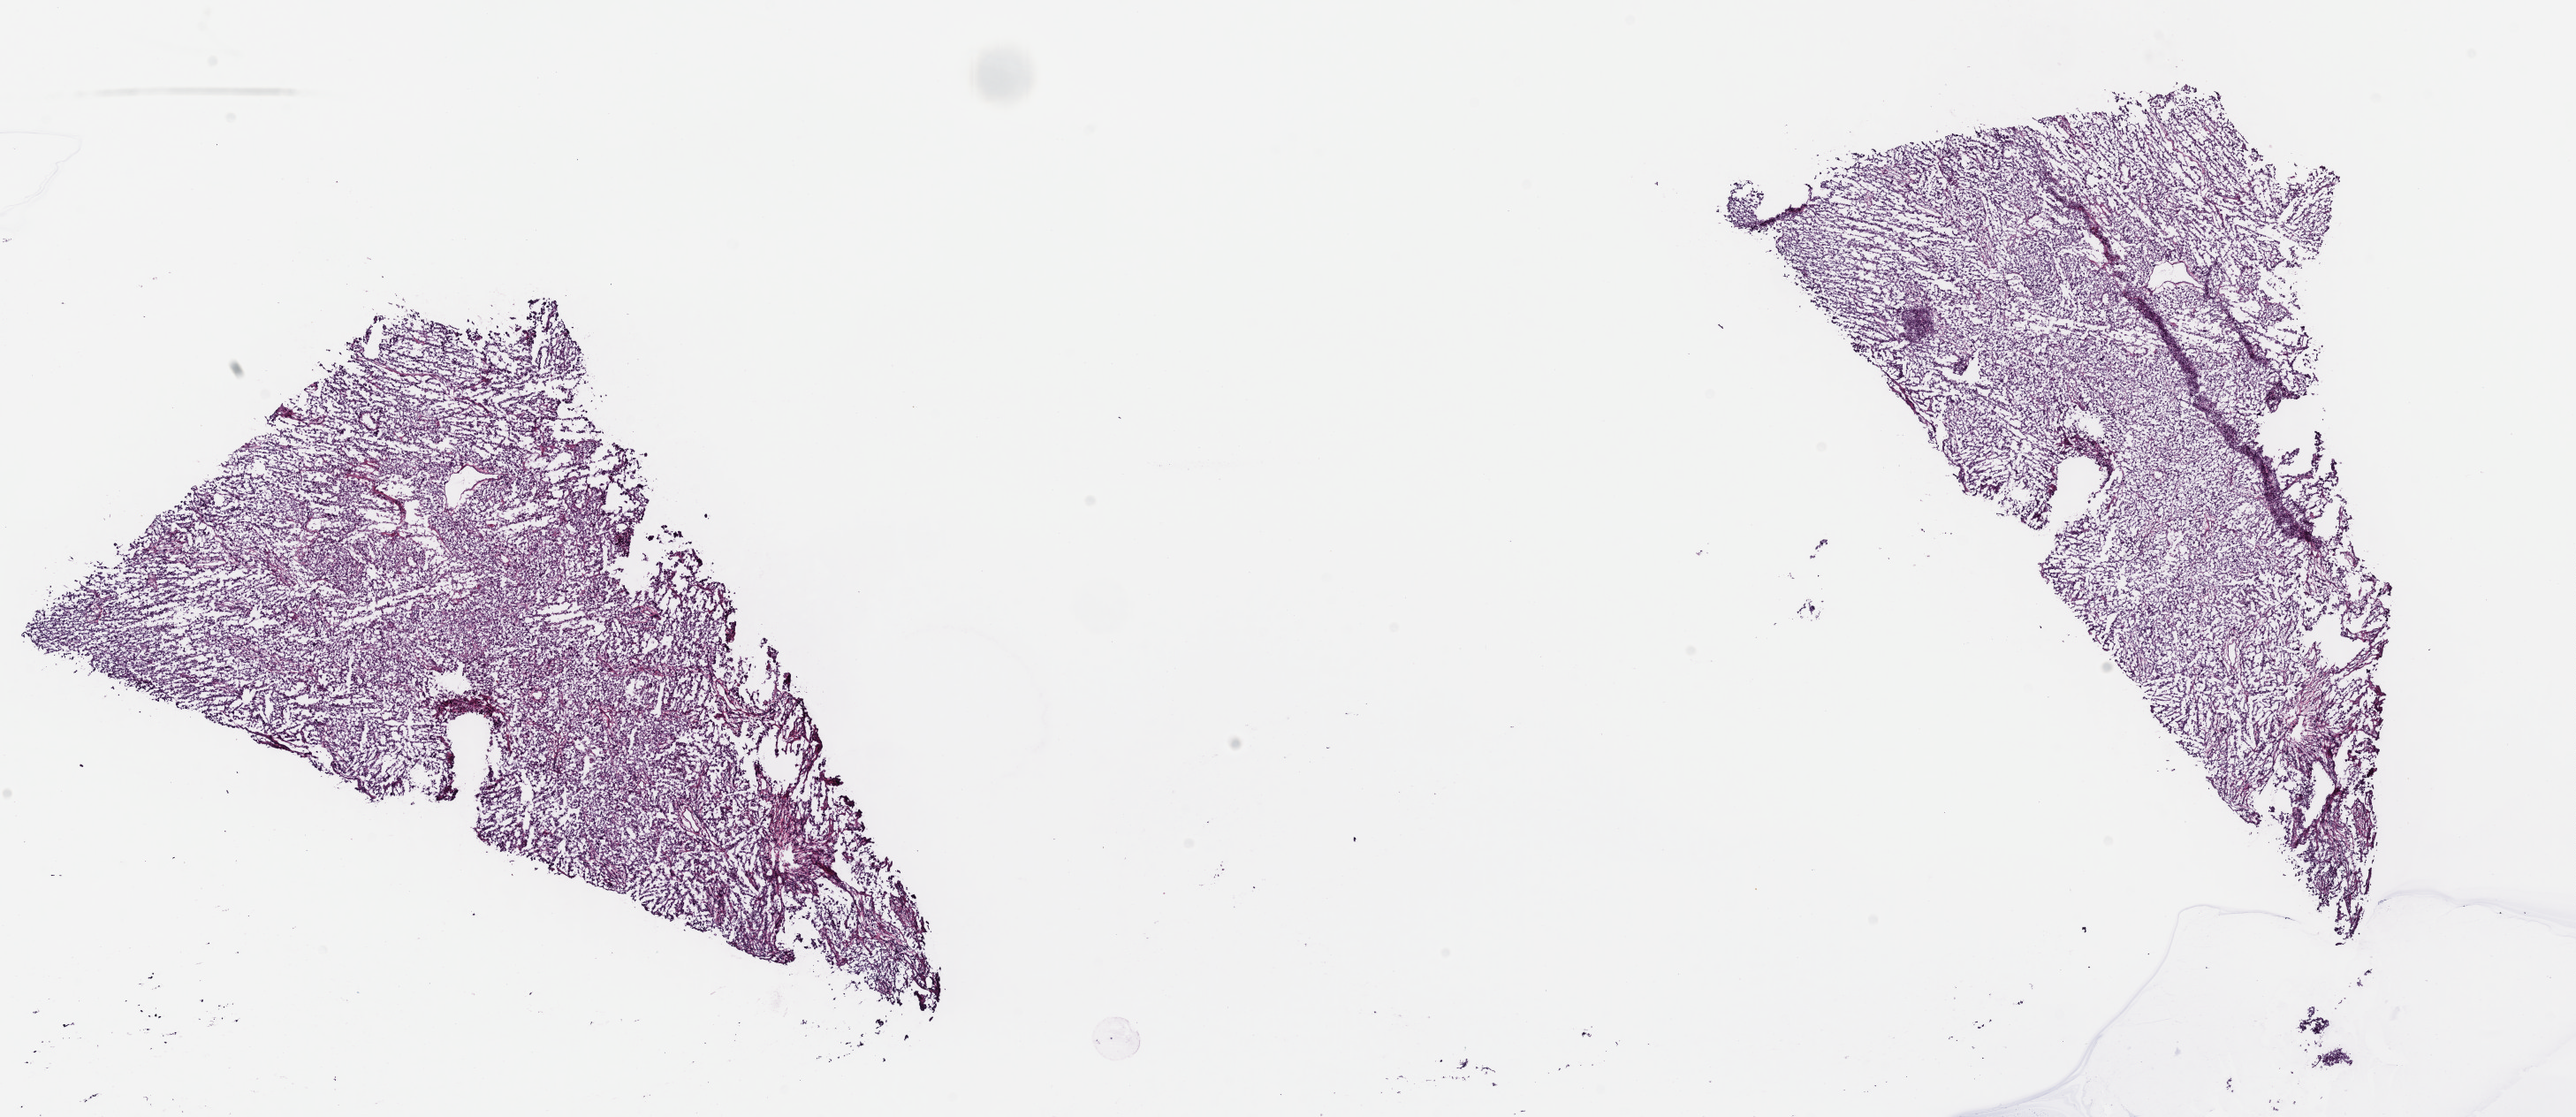
Hematoxylin and eosin (H&E) stained whole-slide image, a low-resolution overview of the entire scanned area, about 23.0 x 10.0 mm; frozen section; metastatic tumour sample. Male patient; age at initial diagnosis 72 years. Slide review estimates, as recorded: tumour cells 85%, tumour nuclei 85%, normal cells 0%, stromal cells 14%, necrosis 1%. Inflammatory infiltration, as recorded: lymphocyte infiltration 3%, monocyte infiltration 2%, neutrophil infiltration 0%.
• this section: metastatic tumour tissue
• patient diagnosis: Malignant melanoma, NOS